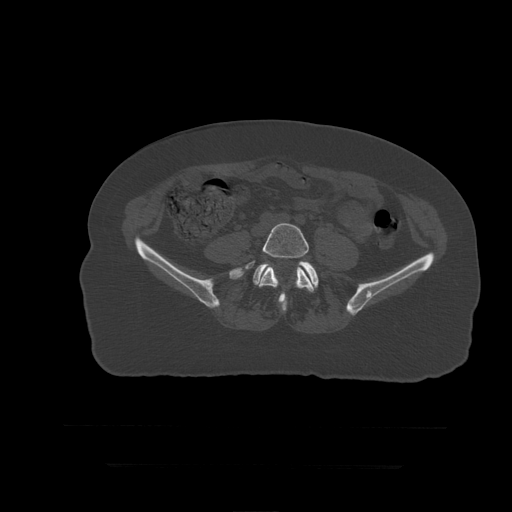
CT including the spine, one axial slice. Position 68 of 399 along the scan axis. Reconstruction kernel STANDARD. Bone window (W 1800 / L 400 HU). 1.25 mm slice thickness. 512 × 512 image matrix. Patient age 41 years. Case-level facts recorded for this patient, not image findings: primary cancer: breast.
Annotated regions visible in this slice (semi-automatic segmentation, software-assisted and operator-edited):
- L5 vertebra: bounding box (x1, y1, x2, y2) in pixels: (245, 223, 315, 303)